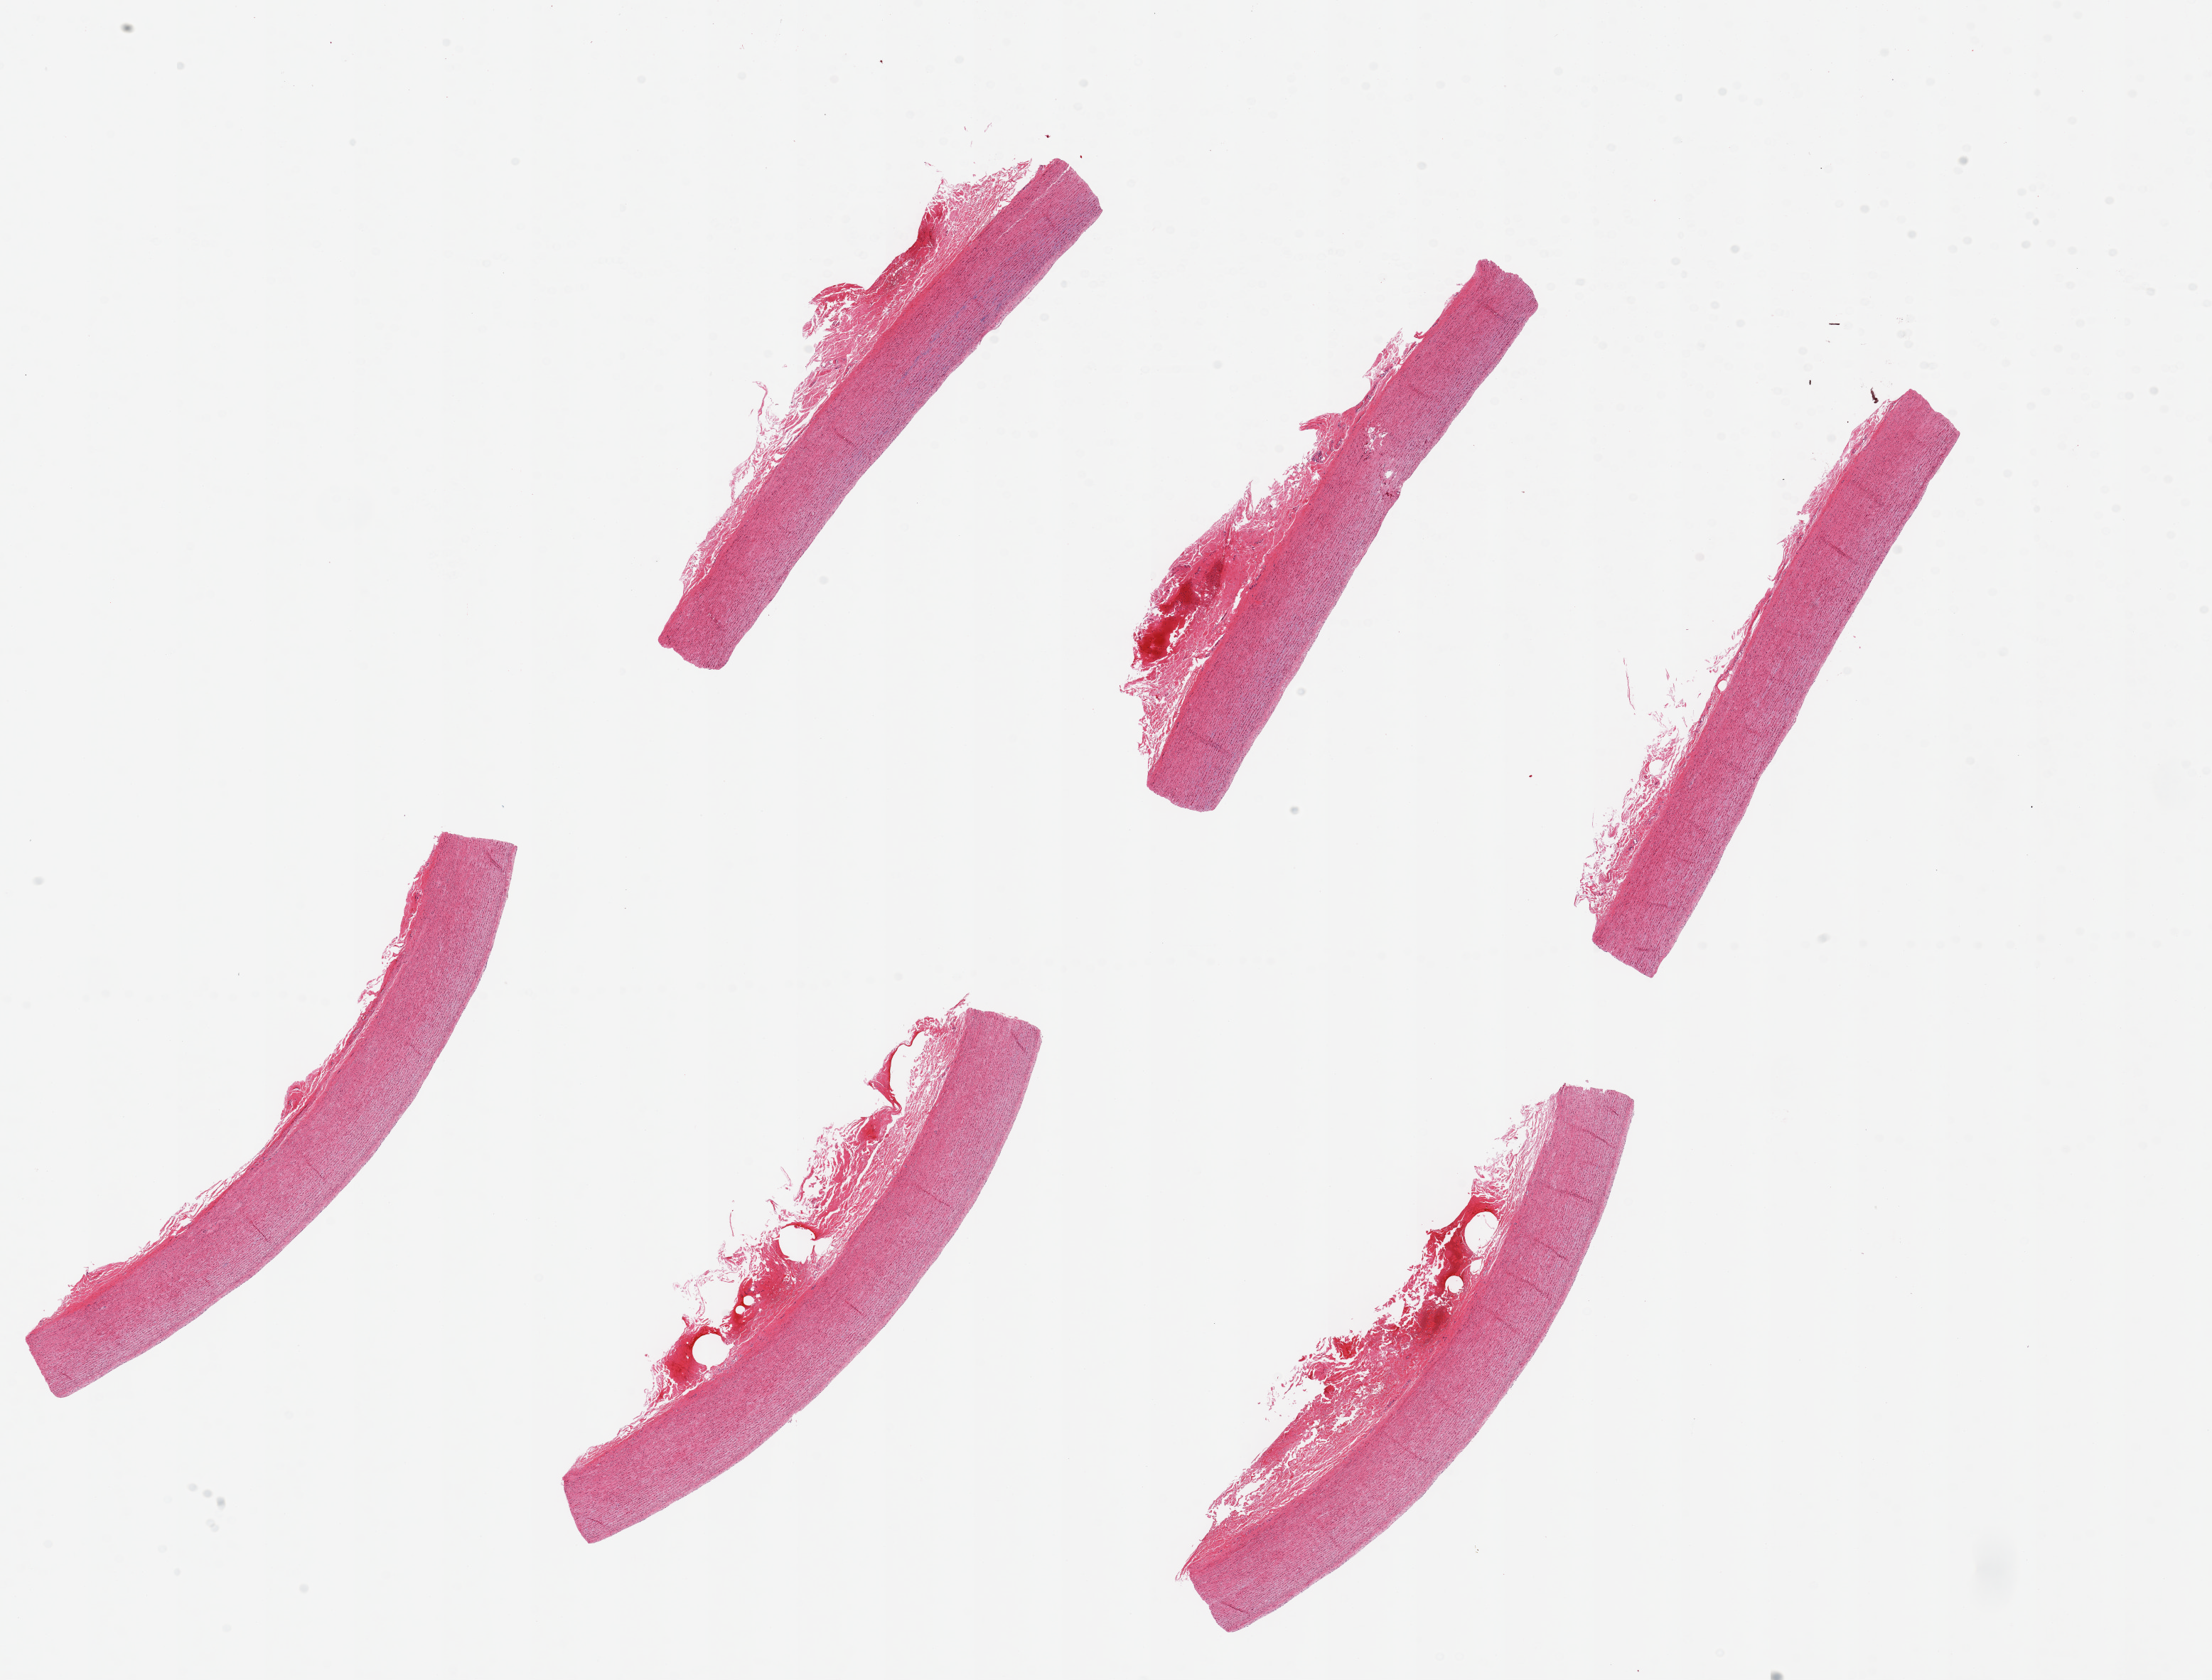
Digitized haematoxylin and eosin-stained section — whole scanned area (about 24.6 x 18.7 mm, from a 20x scan) shown as a low-resolution overview; PAXgene-fixed, paraffin-embedded tissue; sampled site (target tissue): aorta; tissue donor sample. Donor sex: male.
Reviewer comment on this tissue sample: 6 pieces ~7x1mm. Most have ~1mm layer of adentitia/vasa vasorum, deliniated.